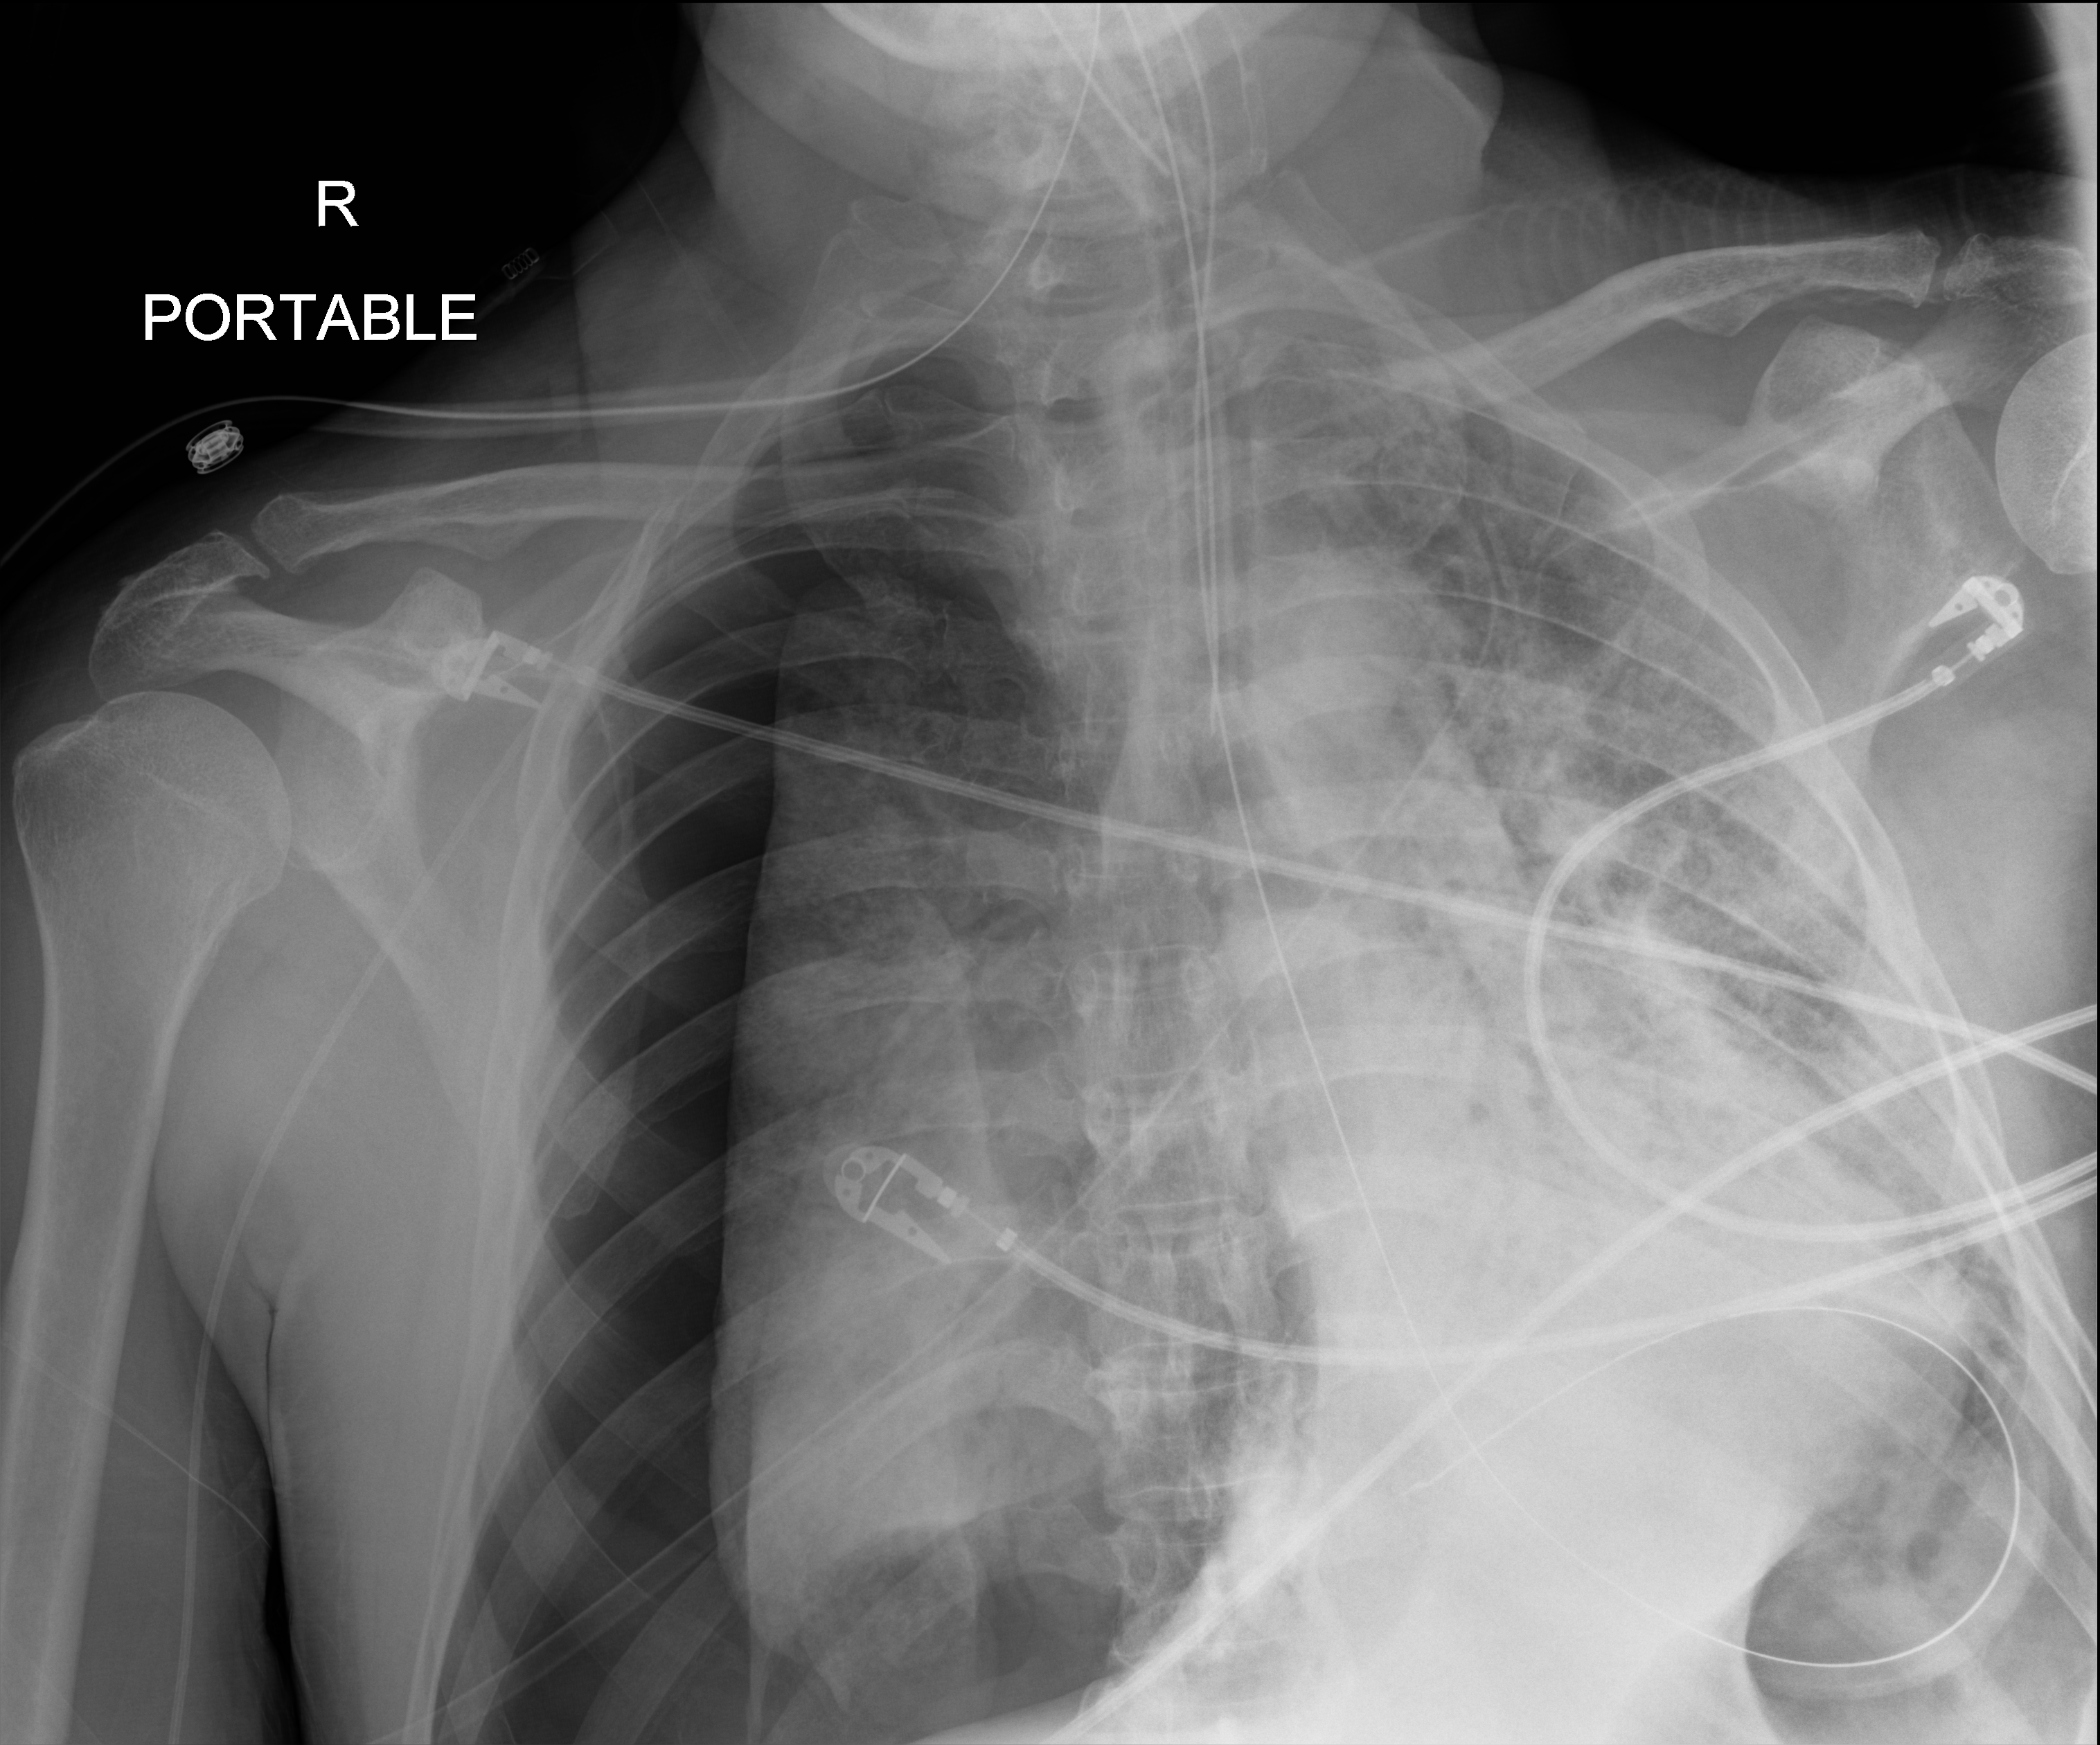
Chest radiograph (digital radiography), anteroposterior (AP) projection. Male patient hospitalised with COVID-19, age 60–74 years.
Admission-level facts for this patient (not findings on this image; timing relative to this image not recorded): hypertension (admission record): yes; admitted to intensive care during this hospital stay: yes; mechanically ventilated during this hospital stay: yes.